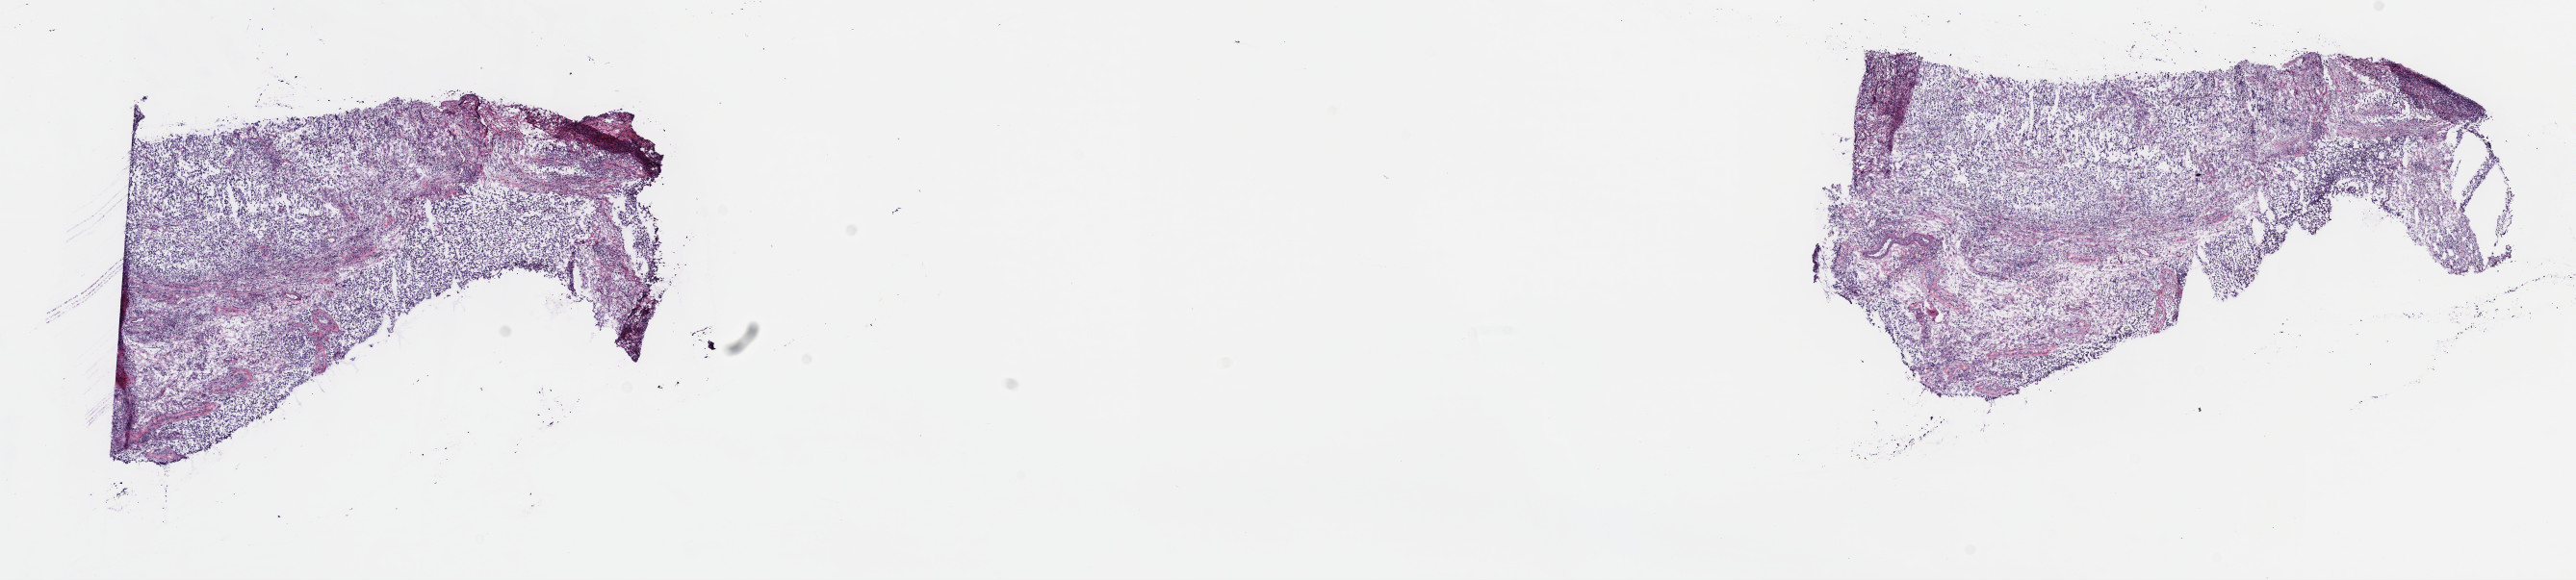
Whole-slide histology image, H&E-stained — low-resolution overview of the scanned area, about 21.6 x 4.9 mm (from a 40x scan); frozen section from the top of the tissue portion; testis, primary tumour sample. Male patient; age at initial diagnosis 33 years. Slide review estimates, as recorded: tumour cells 80%, tumour nuclei 70%, normal cells 0%, stromal cells 20%, necrosis 0%. Infiltration values recorded for this section: lymphocyte infiltration 90%, monocyte infiltration 10%, neutrophil infiltration 0%.
Histologic diagnosis: Seminoma, NOS. Laterality: bilateral. AJCC pathologic stage: IA (6th edition).